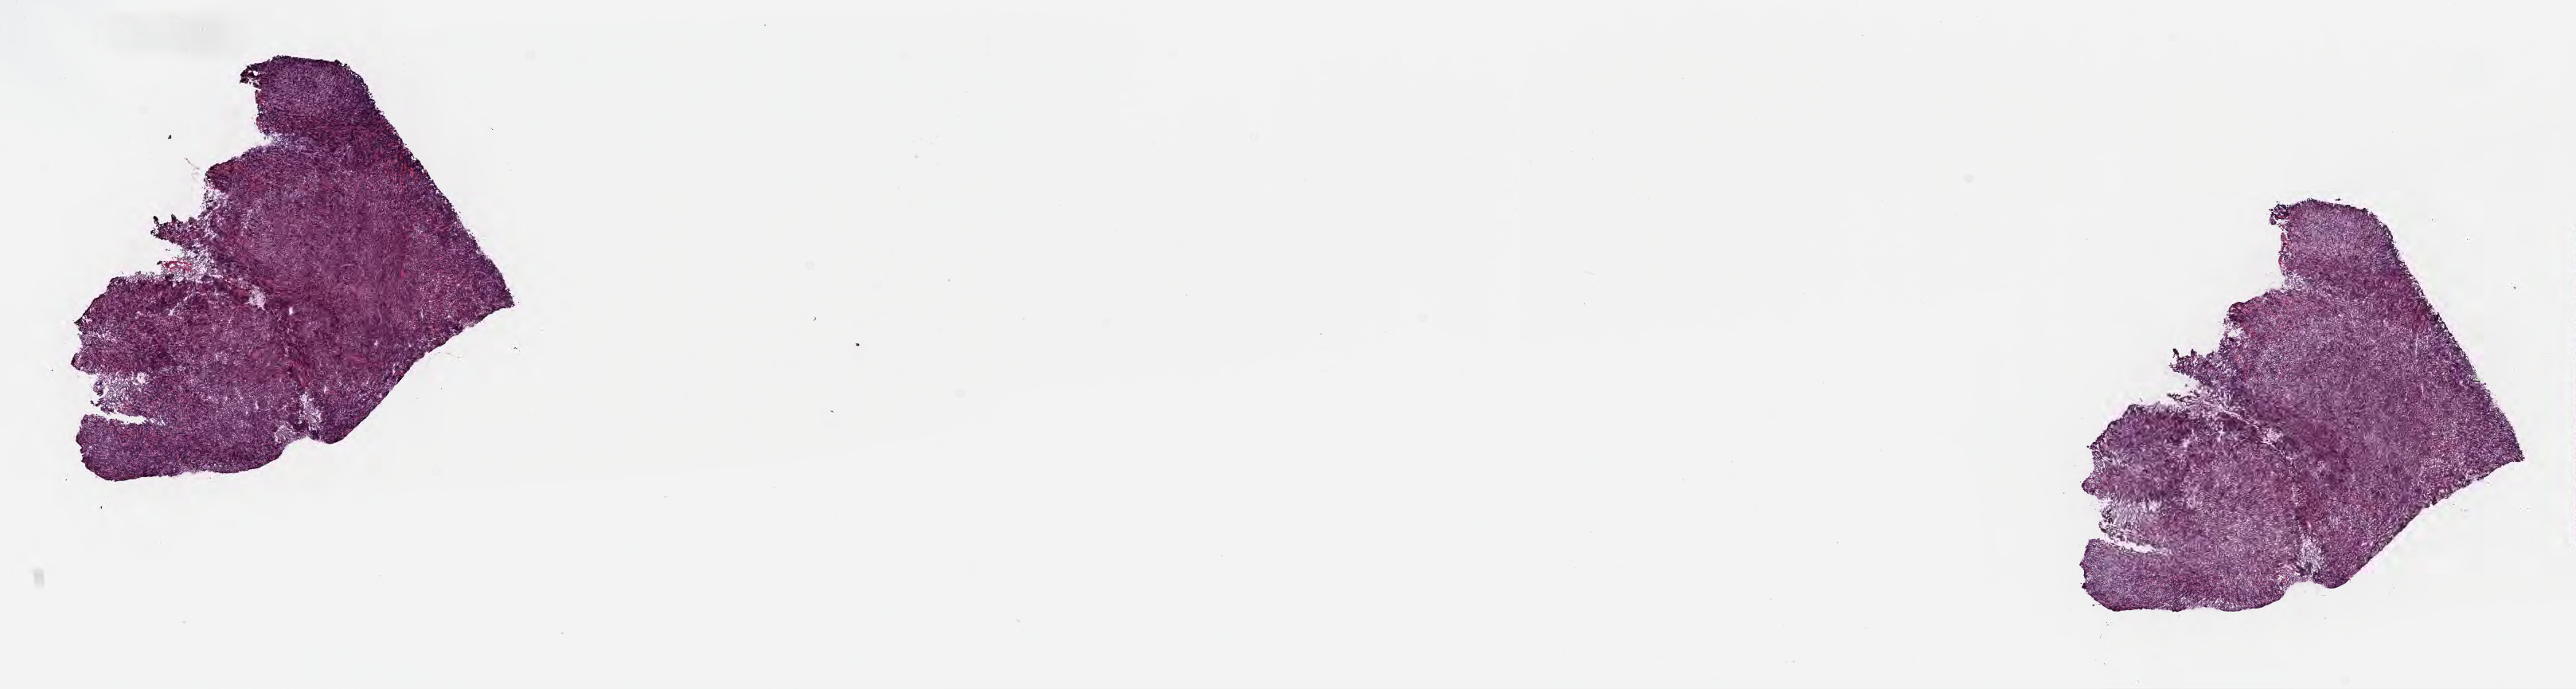
Hematoxylin and eosin (H&E) whole-slide image — whole scanned area (about 26.2 x 7.0 mm) shown as a low-resolution overview, frozen section, primary tumor, site: mandible. Patient: female, age at initial diagnosis 7 years. Pathologist review of this section (percent, as recorded): tumor cells 90%, tumor nuclei 85%, stromal cells 5%, necrosis 5%, normal cells 0%. Inflammatory infiltration, as recorded: lymphocyte infiltration 50%, monocyte infiltration 25%, neutrophil infiltration 5%.
- section: bottom of the tissue portion
- Ann Arbor stage (patient): Stage I
- histologic diagnosis: Burkitt lymphoma, NOS